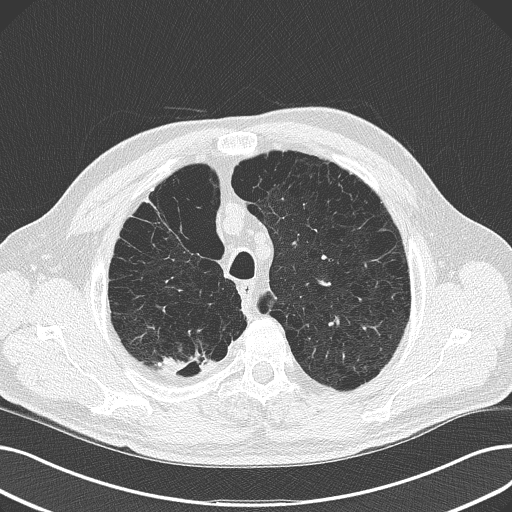
Axial slice from a low-dose chest CT screening exam, second screening round (one year after baseline), lung window (W 1500 / L -600 HU), 120 kVp, 512 × 512 image matrix. Male, age 68 years at enrolment.
Lesion marked by an expert reader, box from (x=143, y=333) to (x=225, y=391) px. The screening reader recorded 4 non-calcified nodules or masses ≥4 mm on this exam (right upper lobe, left lower lobe, left upper lobe, right lower lobe); which of them this box marks is not recorded. Official screen result: positive, other.